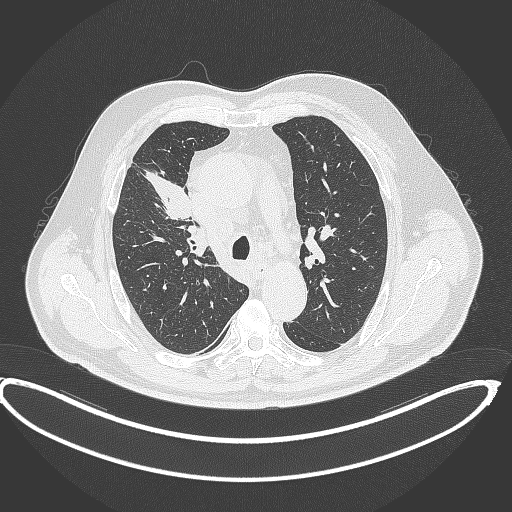
Chest CT, one axial slice. Position 282 of 390 along the scan axis. Lung window (W 1500 / L -600 HU). 1 mm slice thickness. 512 × 512 image matrix, field of view 448 × 448 mm. Patient: male, 62 years. Case-level facts recorded for this patient, not image findings: clinical TNM (as recorded): T1c N3 M1c.
Annotated regions visible in this slice (rectangle marked by the reading radiologist):
- lung tumour (recorded histology: adenocarcinoma): bounding box (x1, y1, x2, y2) in pixels: (140, 166, 195, 220)